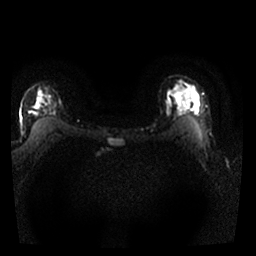
Breast MRI, one axial slice. Position 20 of 25 along the scan axis. Diffusion-weighted series; image 2 of 4 stored at this slice position (different b-values; order by instance number). 1.5 T. 256 × 256 image matrix, field of view 300 × 300 mm. Female patient.
Annotated regions visible in this slice (expert manual segmentation):
- tumour on diffusion-weighted imaging: box from (x=165, y=96) to (x=175, y=117) px